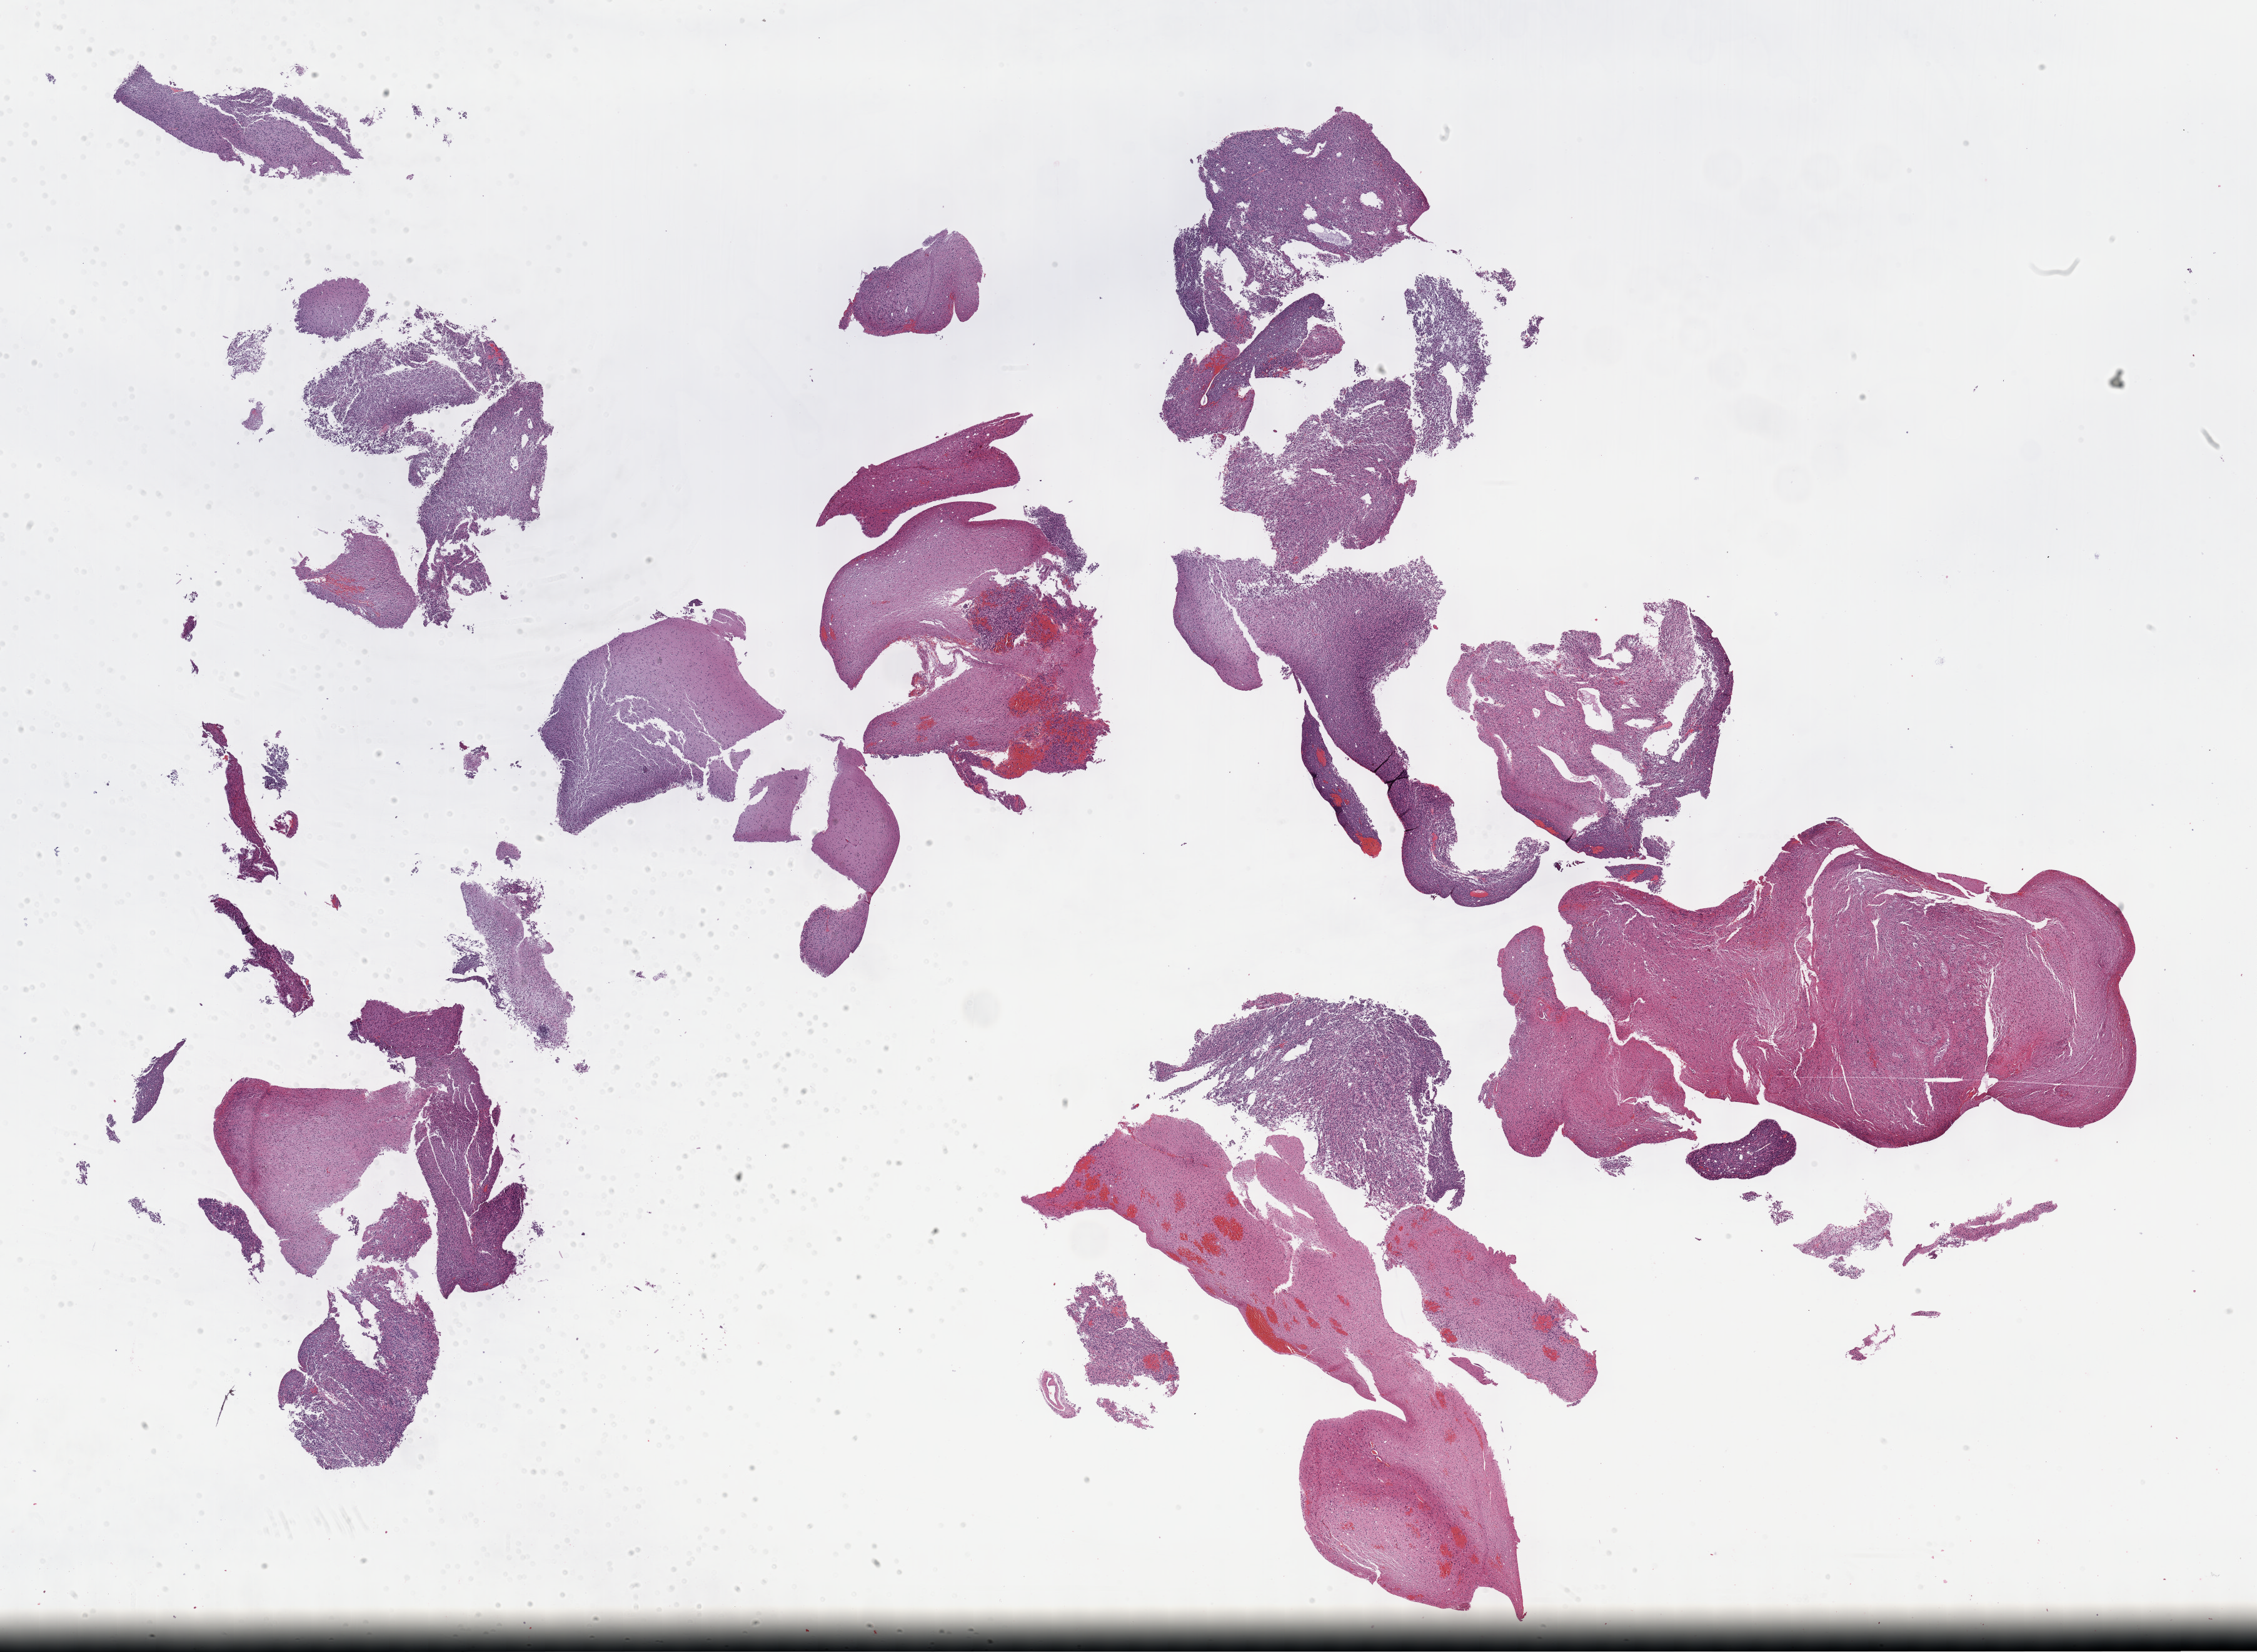
H&E-stained whole-slide image, shown as a low-resolution overview of the whole scanned area (about 29.2 x 21.4 mm, slide scanned at 40x). Formalin-fixed paraffin-embedded (FFPE) diagnostic section. Sample: primary tumour, brain. Female patient; age at initial diagnosis 44 years.
Diagnosis: Astrocytoma, anaplastic.